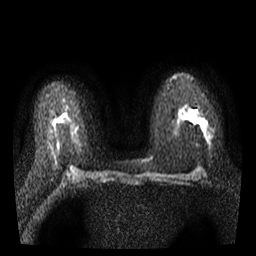
Breast MRI, one axial slice. Position 18 of 35 along the scan axis. Diffusion-weighted series; image 2 of 4 stored at this slice position (different b-values; order by instance number). 3 T. 5 mm slice thickness. 256 × 256 image matrix, field of view 300 × 300 mm. Female patient.
Outlined on this slice (manually delineated by an expert):
- tumour on diffusion-weighted imaging: bounding box (x1, y1, x2, y2) in pixels: (190, 115, 202, 132)